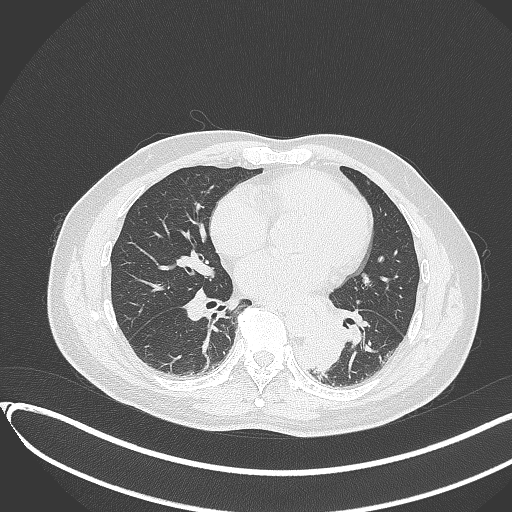
Chest CT, one axial slice. Slice 148 of 417 in the series (ordered by position). Reconstruction kernel B70f. 120 kVp. Lung window (W 1500 / L -600 HU). 1 mm slice thickness. 512 × 512 image matrix. Patient: male, 54 years. Case-level facts recorded for this patient, not image findings: clinical TNM (as recorded): T3 N0 M0.
Structures marked on this image (rectangle marked by the reading radiologist):
- lung tumour (recorded histology: squamous cell carcinoma): bounding box <297,323,344,374> (left, top, right, bottom; pixels)